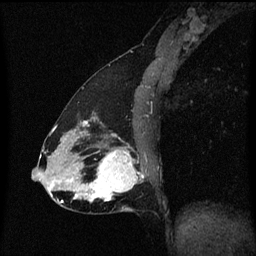
Breast MRI (dynamic contrast-enhanced), one sagittal slice; position 27 of 60 along the scan axis; dynamic contrast-enhanced series, image 2 of 3 at this slice position (ordered by acquisition); 1.5 T; TE 4.2 ms, TR 8.4 ms; 2 mm slice thickness; 256 × 256 image matrix. Female patient, age 47 years.
Structures marked on this image (semi-automatic segmentation, software-assisted and operator-edited):
- analysis volume of interest (the breast-tissue region the enhancement analysis was run in; not a lesion): box from (x=81, y=138) to (x=146, y=215) px
- tumour enhancement mask (voxels above the 70 % enhancement threshold inside the analysis volume of interest): (x=85, y=150)–(x=142, y=203)